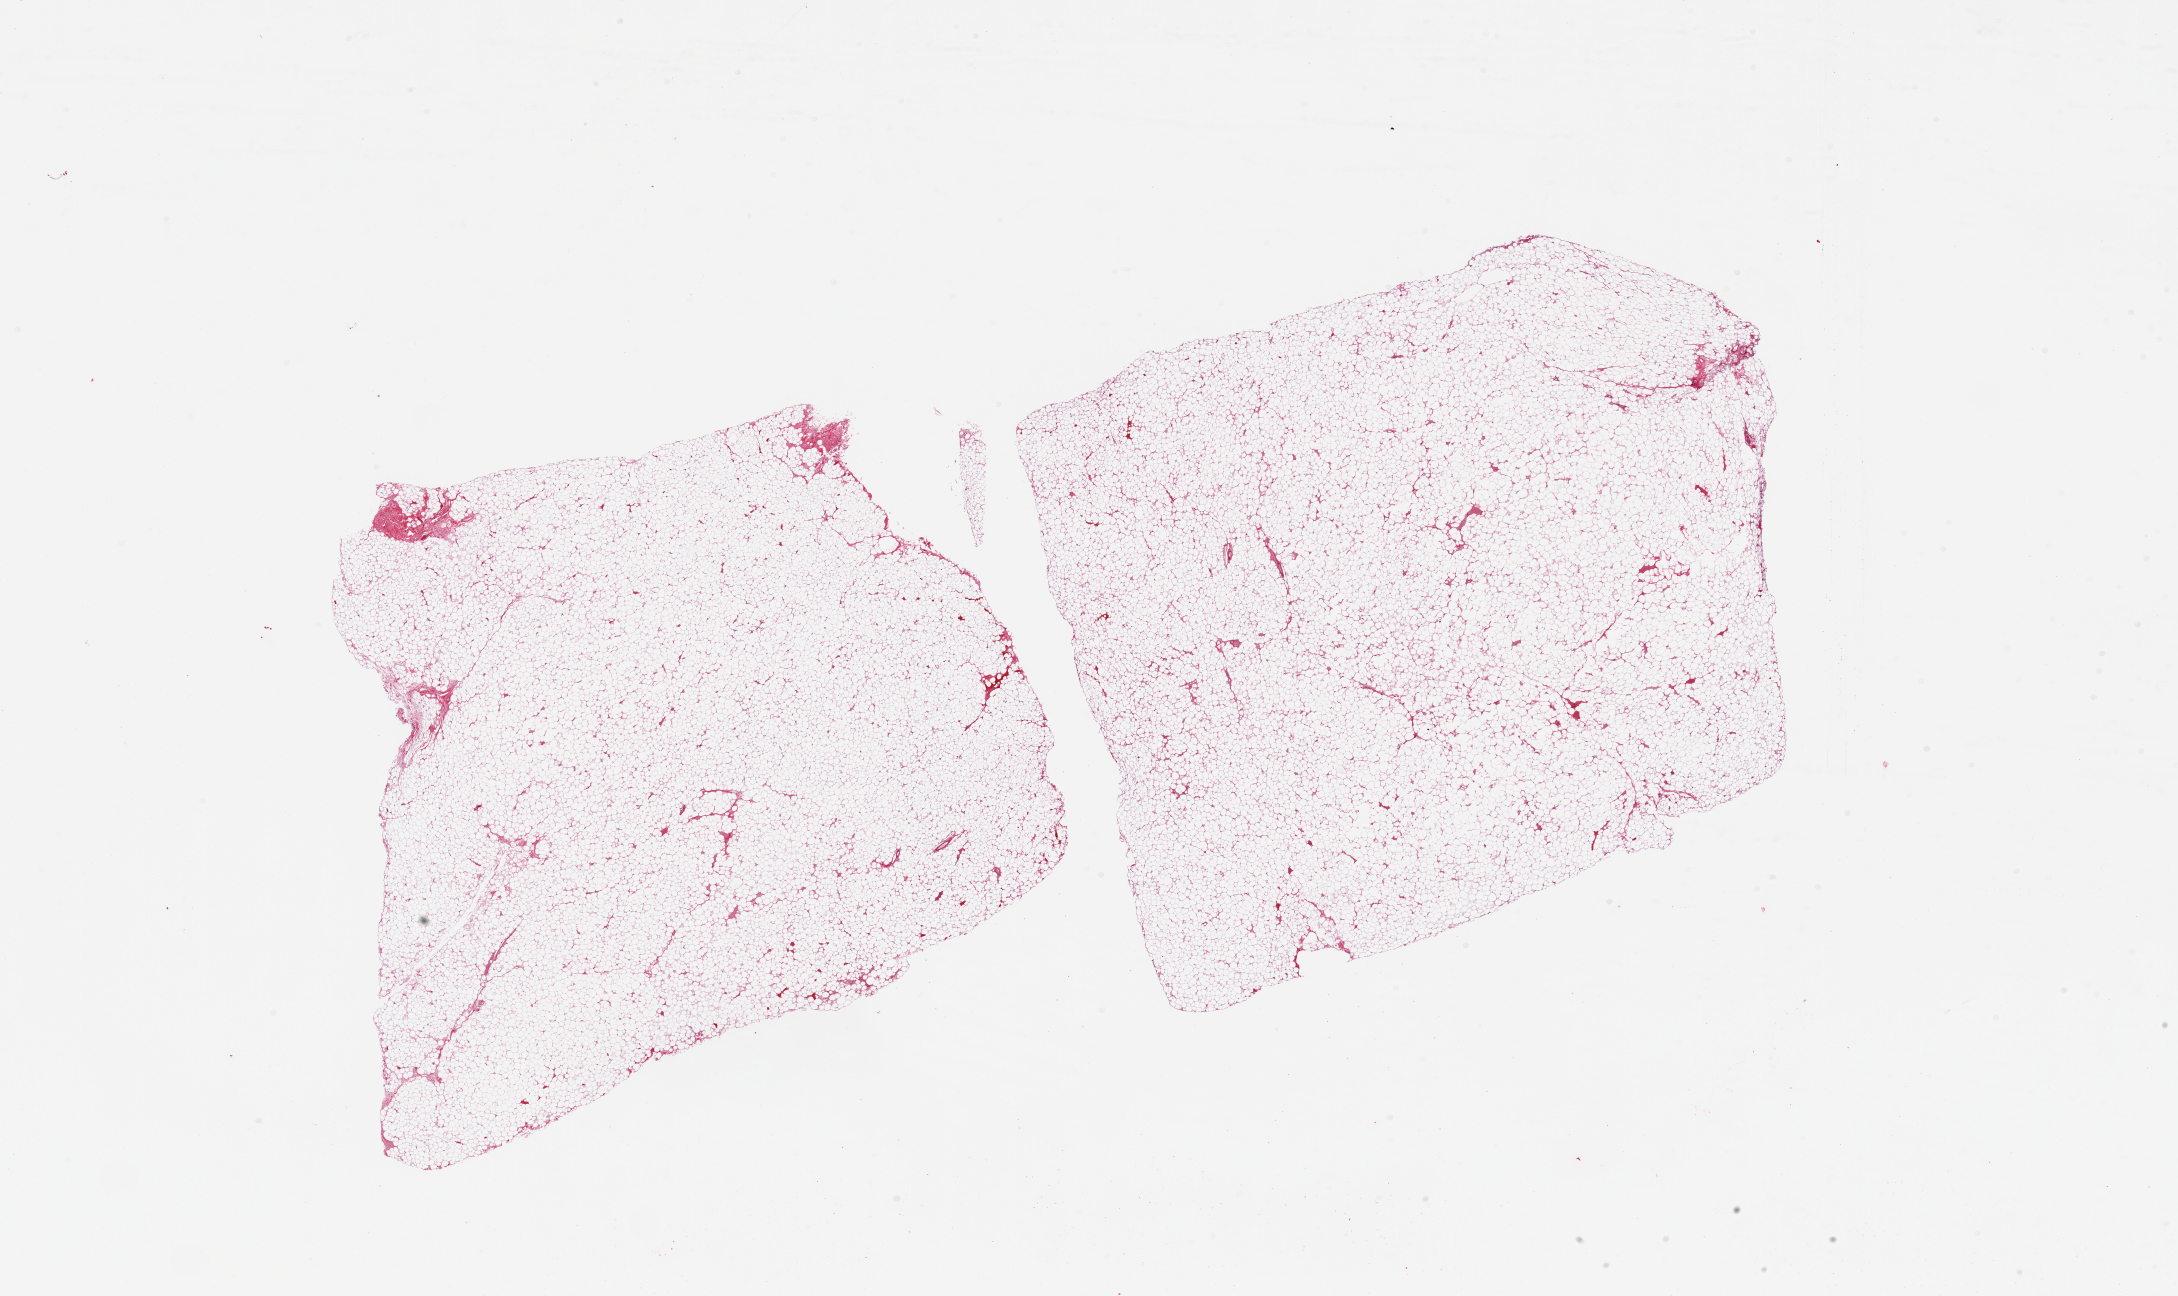
Haematoxylin and eosin whole-slide image, brightfield — whole scanned area (about 34.5 x 20.5 mm) shown as a low-resolution overview; PAXgene-fixed, paraffin-embedded tissue; section of adrenal gland (target tissue); tissue donor sample.
- review note (as recorded): 2 pieces of fat without any adrenal tissue